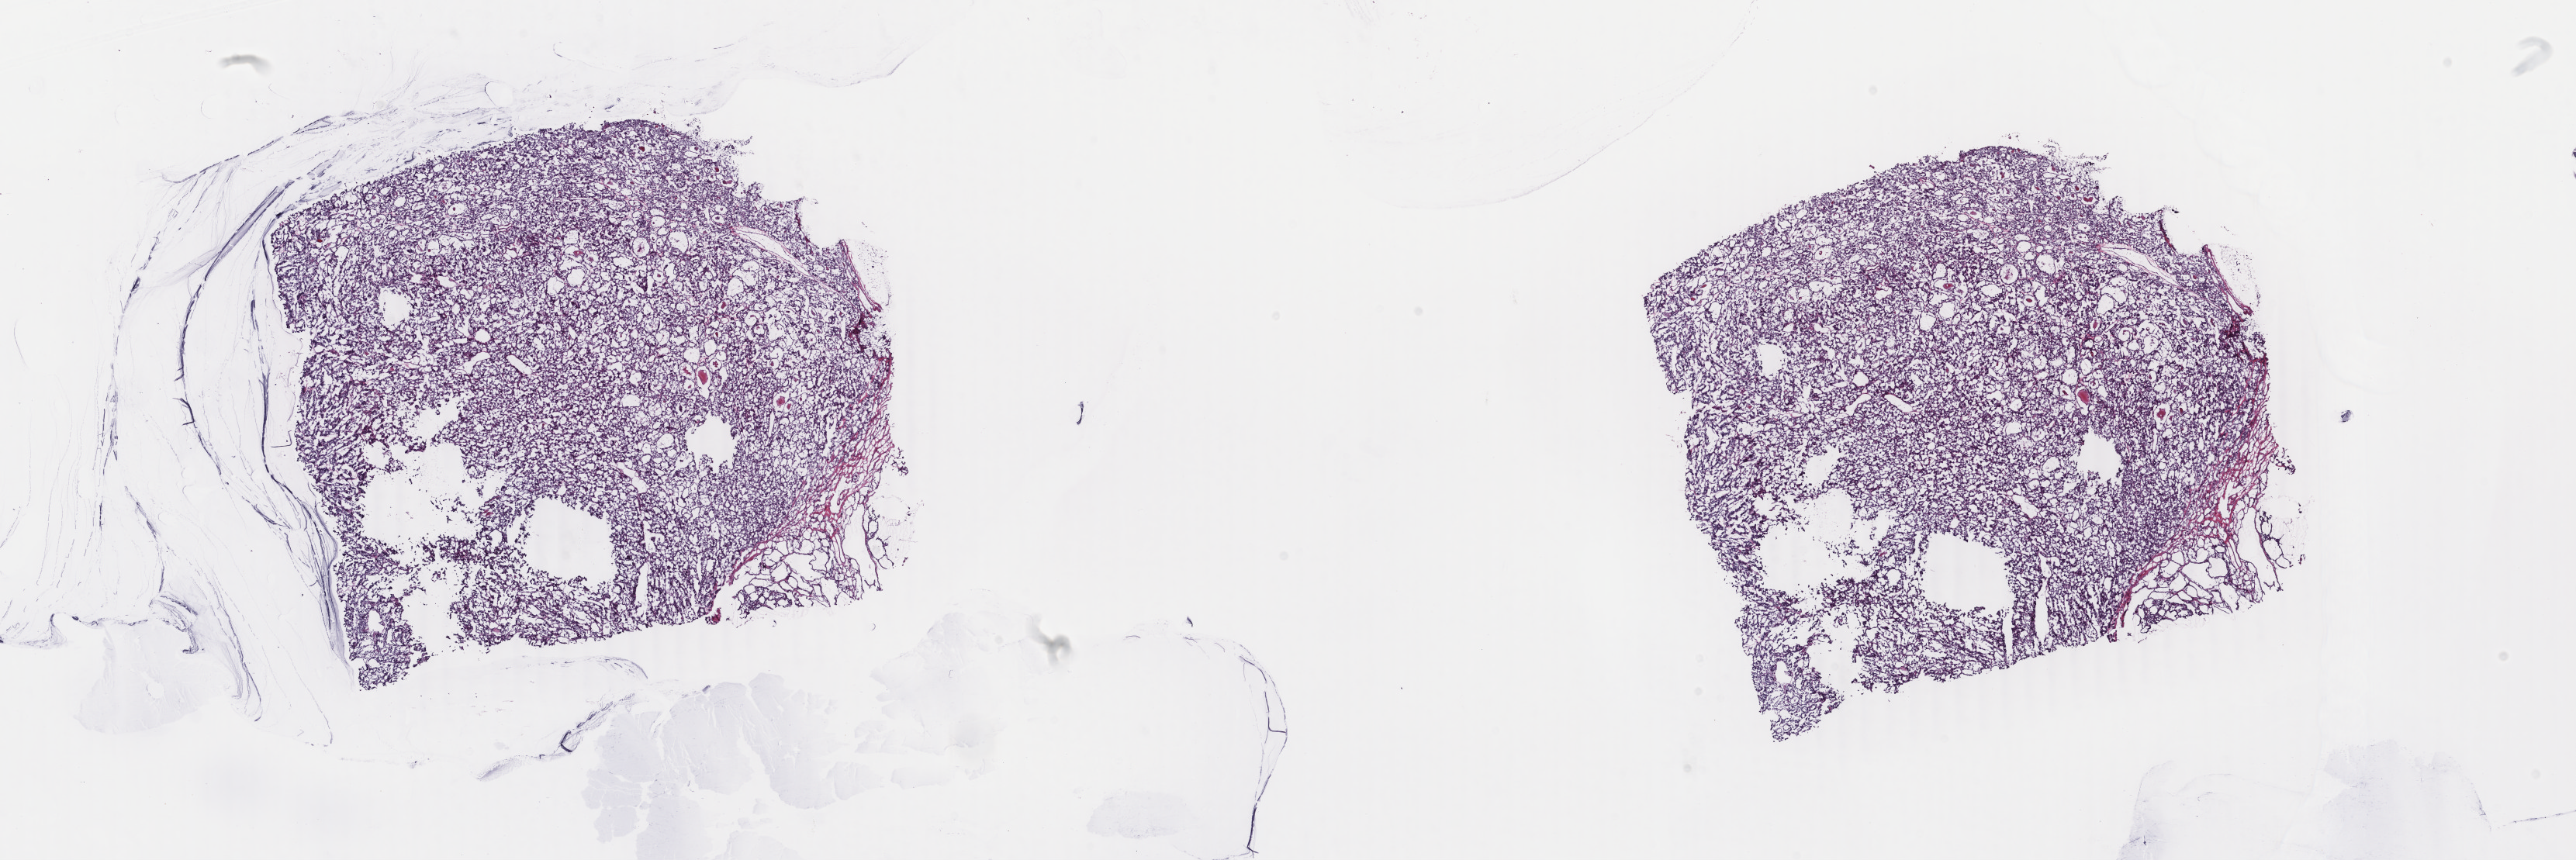
Digitized H&E-stained tissue section (whole slide), low-resolution overview of the scanned area, about 26.4 x 8.8 mm; frozen section; sample: primary tumour, thyroid. Male patient; age at initial diagnosis 29 years. Composition of this section per pathologist review: tumour cells 90%, tumour nuclei 90%, normal cells 0%, stromal cells 10%, necrosis 0%. Infiltration values recorded for this section: lymphocyte infiltration 1%, monocyte infiltration 0%, neutrophil infiltration 0%.
Diagnosis: Papillary adenocarcinoma, NOS (thyroid gland). Laterality: bilateral. Lymph nodes positive (case pathology): 0 of 5 examined. AJCC pathologic stage: I (7th edition). TNM: T1b N0 MX.